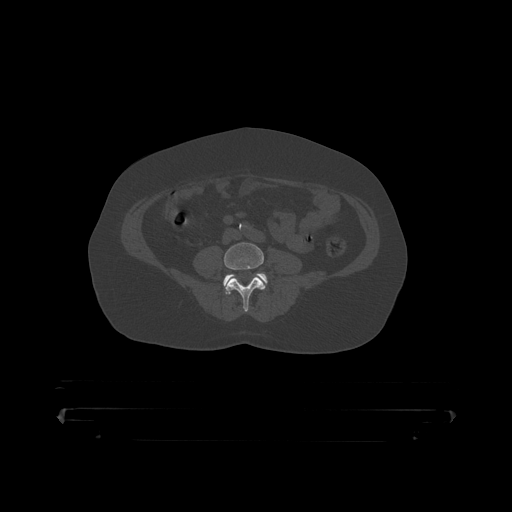
CT including the spine, one axial slice. Slice 58 of 390 in the series (ordered by position). Reconstruction kernel STANDARD. 120 kVp. Bone window (W 1800 / L 400 HU). 1.25 mm slice thickness. 512 × 512 image matrix, field of view 650 × 650 mm. Male patient, age 60 years. Case-level facts recorded for this patient, not image findings: primary cancer: prostate.
Outlined on this slice (semi-automatic segmentation, software-assisted and operator-edited):
- L4 vertebra: bounding box (x1, y1, x2, y2) in pixels: (225, 243, 265, 312)
- L5 vertebra: (223, 273, 268, 288)